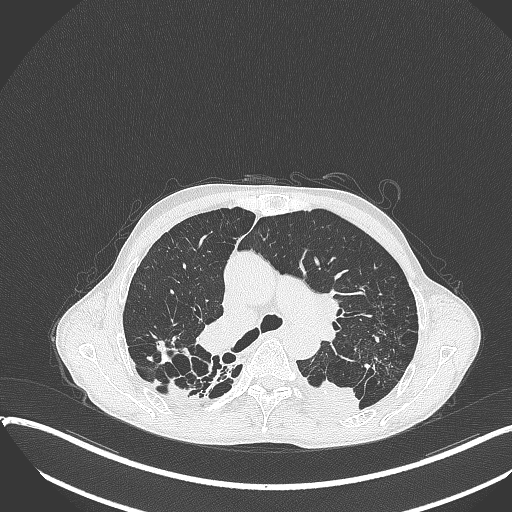
Chest CT, one axial slice. Slice 250 of 401 in the series (ordered by position). Reconstruction kernel B70f. 120 kVp. Lung window (W 1500 / L -600 HU). 1 mm slice thickness. 512 × 512 image matrix. Male patient, age 57 years. From the clinical record (not read from this slice): clinical TNM (as recorded): T4 N0 M0.
Outlined on this slice (rectangle marked by the reading radiologist):
- lung tumour (recorded histology: squamous cell carcinoma): bounding box [x1, y1, x2, y2] px = [301, 369, 362, 419]